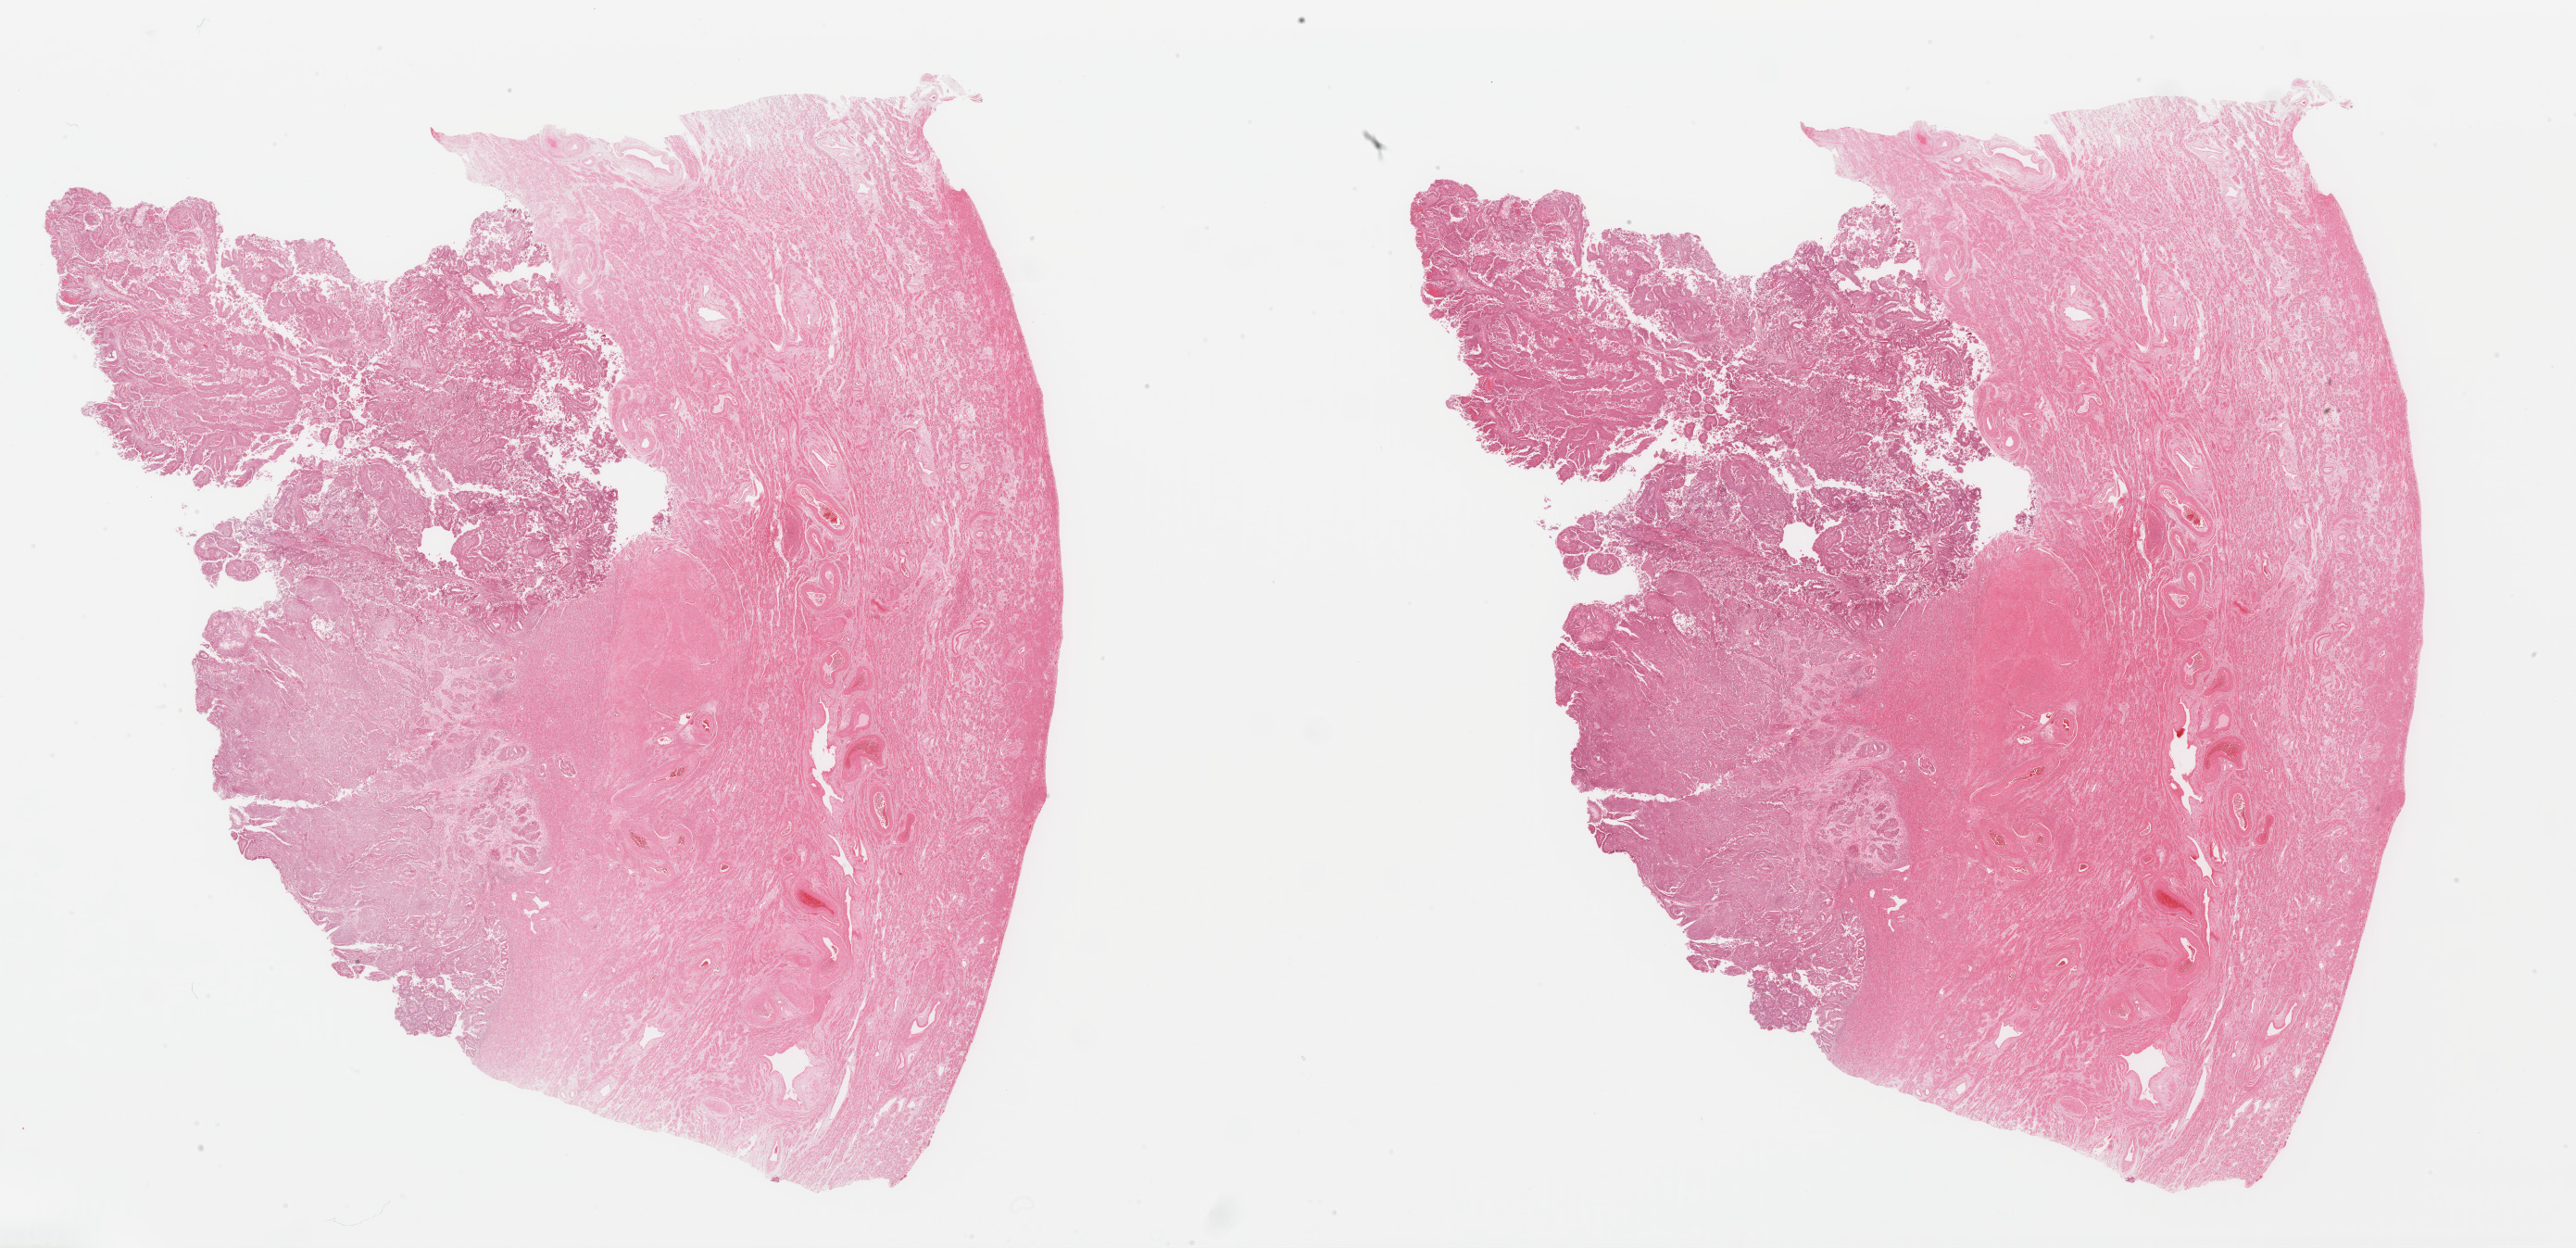
H&E whole-slide image, shown as a low-resolution overview of the whole scanned area (about 43.9 x 21.3 mm, slide scanned at 40x), FFPE section, sample: primary tumour, uterus. Female, age 67 years at initial diagnosis. Histologic grade: G3 (poorly differentiated).
Lymph nodes positive (case pathology): 0 of 9 examined. Pathologic diagnosis: Serous cystadenocarcinoma, NOS. FIGO stage: IIIA.